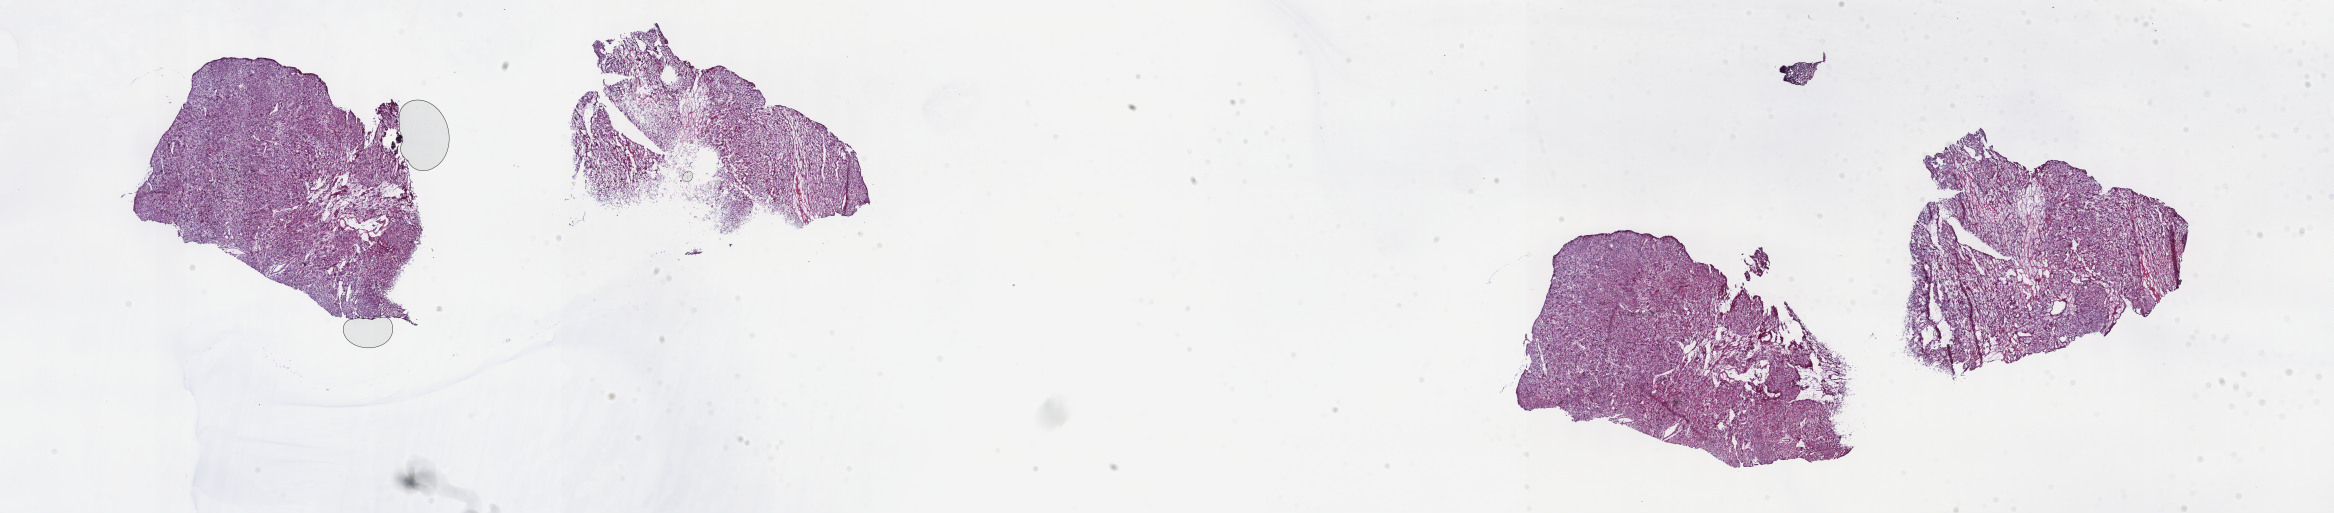
Whole-slide histology image, Hematoxylin and eosin (H&E) stained — low-resolution overview of the scanned area, about 37.8 x 8.3 mm (from a 40x scan). Frozen section from the top of the tissue portion. Connective, subcutaneous and other soft tissues, primary tumour sample. Patient: female, age at initial diagnosis 56 years. Composition of this section per pathologist review: tumour cells 100%, tumour nuclei 80%, normal cells 0%, stromal cells 0%, necrosis 0%. Infiltration values recorded for this section: lymphocyte infiltration 1%, monocyte infiltration 0%, neutrophil infiltration 0%.
- diagnosis: Leiomyosarcoma, NOS